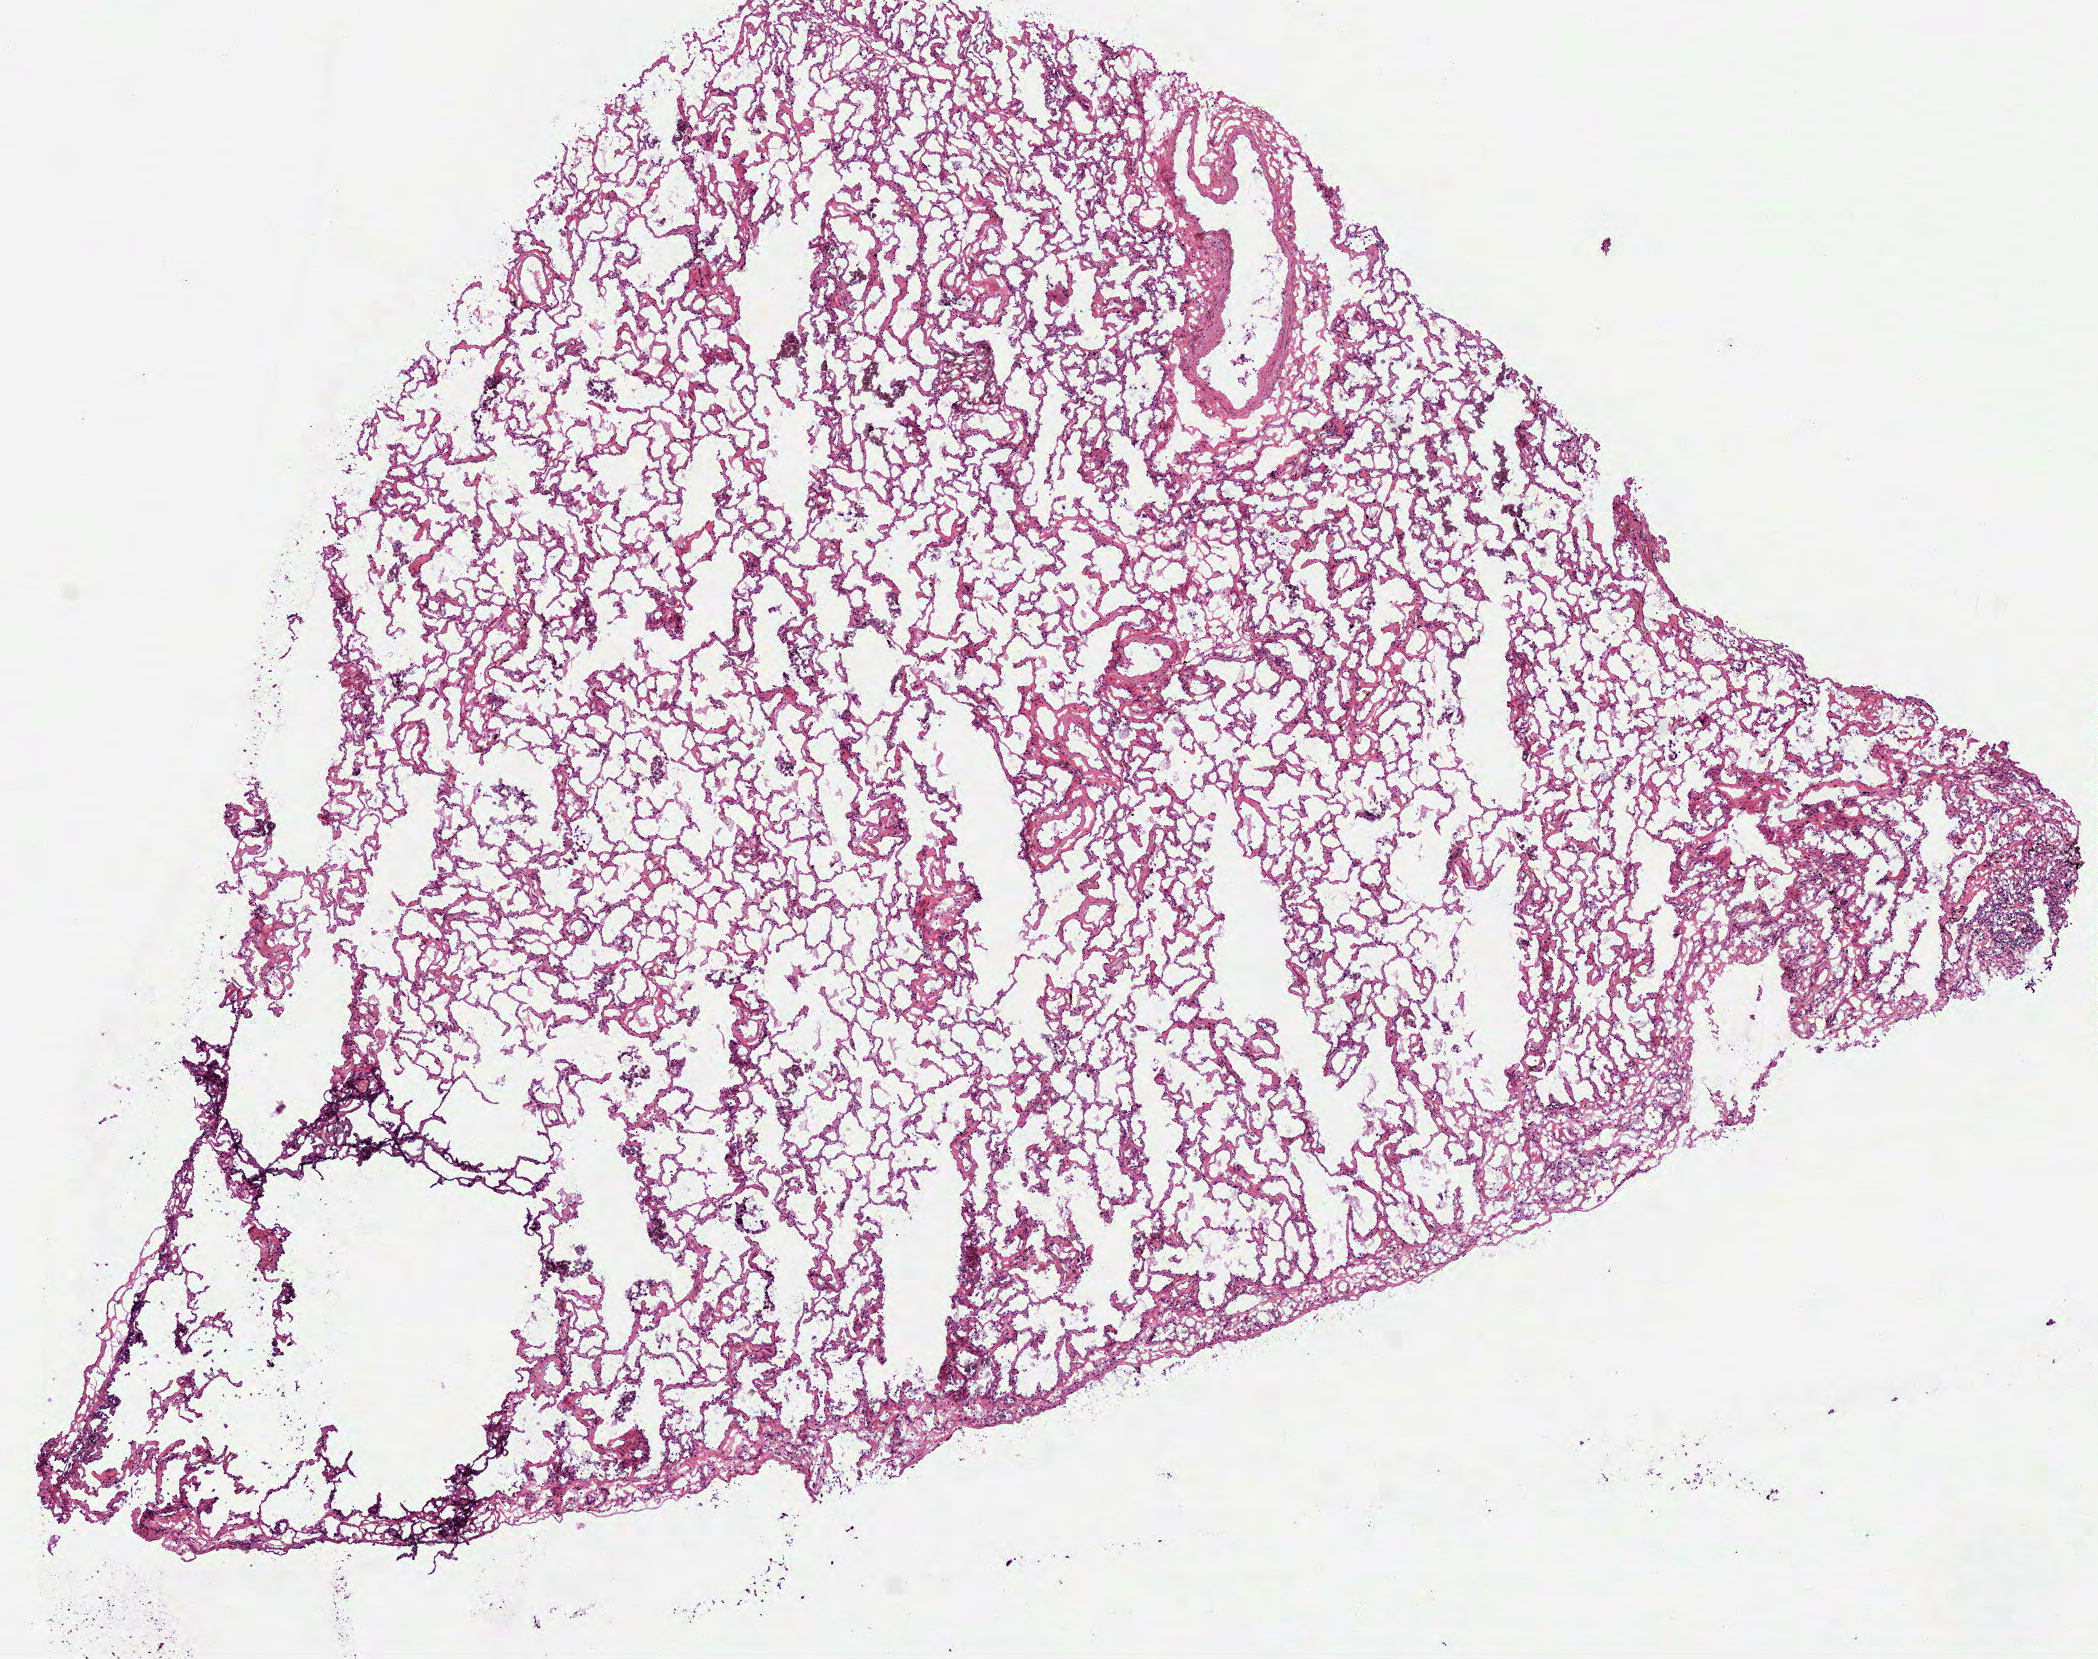
H&E-stained whole-slide image, whole scanned area (about 8.5 x 6.7 mm) shown as a low-resolution overview; frozen section from the top of the tissue portion; solid tissue normal (non-tumour tissue) sample from the lung. Female patient; age at initial diagnosis 46 years.
* this section: solid tissue normal (non-tumour) sample from the same patient
* patient diagnosis: Adenocarcinoma, NOS (middle lobe, lung)